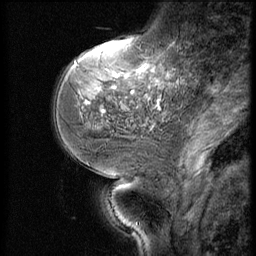
Breast MRI (dynamic contrast-enhanced), one sagittal slice; position 19 of 56 along the scan axis; dynamic contrast-enhanced series, image 2 of 3 at this slice position (ordered by acquisition); 1.5 T; TE 4.2 ms, TR 9 ms; 256 × 256 image matrix, field of view 180 × 180 mm. Female patient, age 51 years. From the clinical record (not read from this slice): setting: breast cancer imaged before/during neoadjuvant chemotherapy; receptor status: triple-negative.
Outlined on this slice (semi-automatically segmented with operator editing):
- analysis volume of interest (the breast-tissue region the enhancement analysis was run in; not a lesion): bounding box [x1, y1, x2, y2] px = [73, 46, 172, 147]
- tumour enhancement mask (voxels above the 140 % enhancement threshold inside the analysis volume of interest): [139, 70, 143, 73]